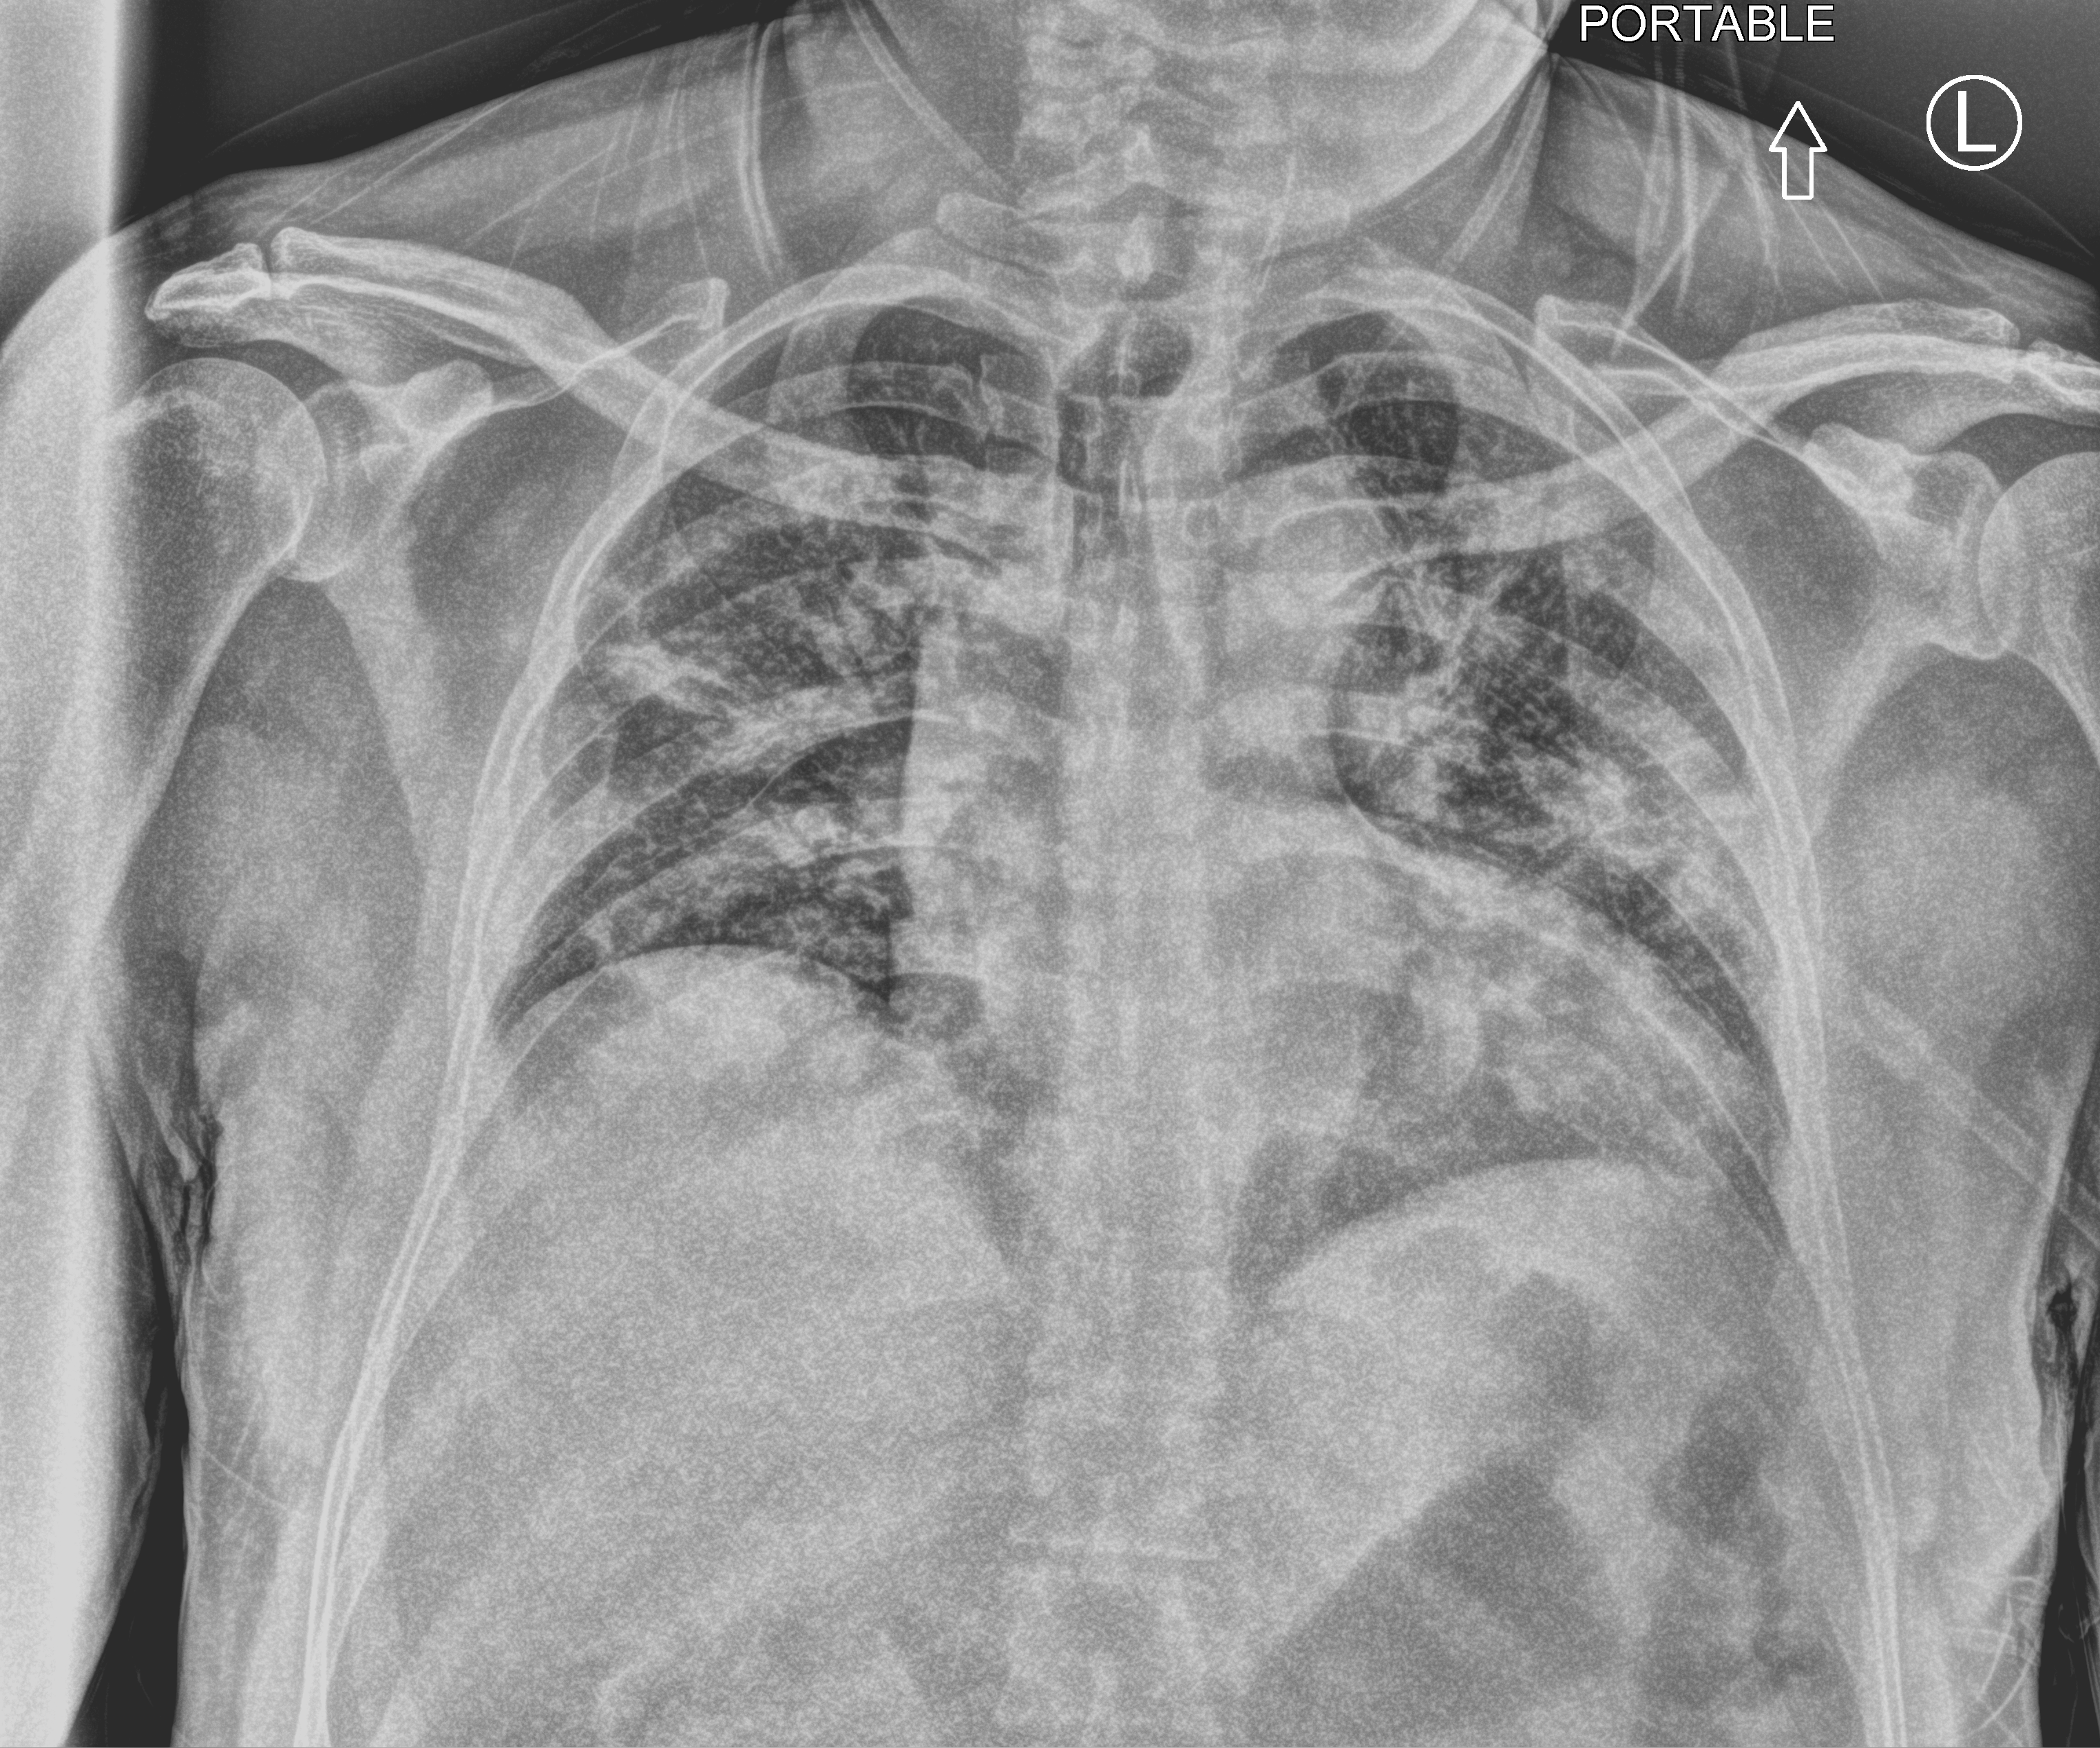
Portable chest radiograph. Male patient hospitalised with COVID-19, age 18–59 years.
Hospital-stay facts (about this admission, not read from this image; timing relative to this image not recorded):
- admitted to intensive care during this hospital stay: no